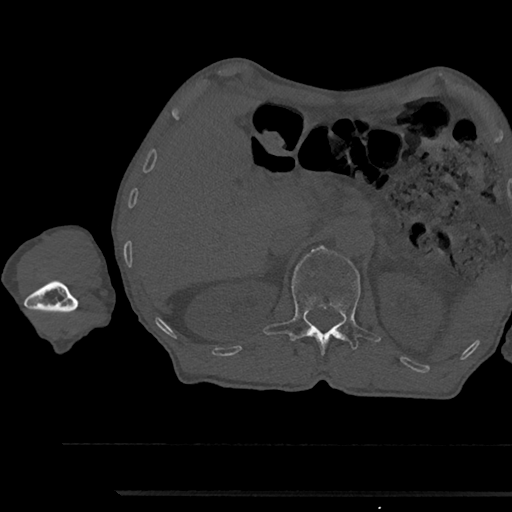
CT including the spine, one axial slice; 120 kVp; bone window (W 1800 / L 400 HU); 0.5 mm slice thickness; 512 × 512 image matrix. Patient: male, 79 years. From the clinical record (not read from this slice): primary cancer: prostate.
Structures marked on this image (semi-automatically segmented with operator editing):
- L1 vertebra: bounding box (x1, y1, x2, y2) in pixels: (263, 245, 380, 357)